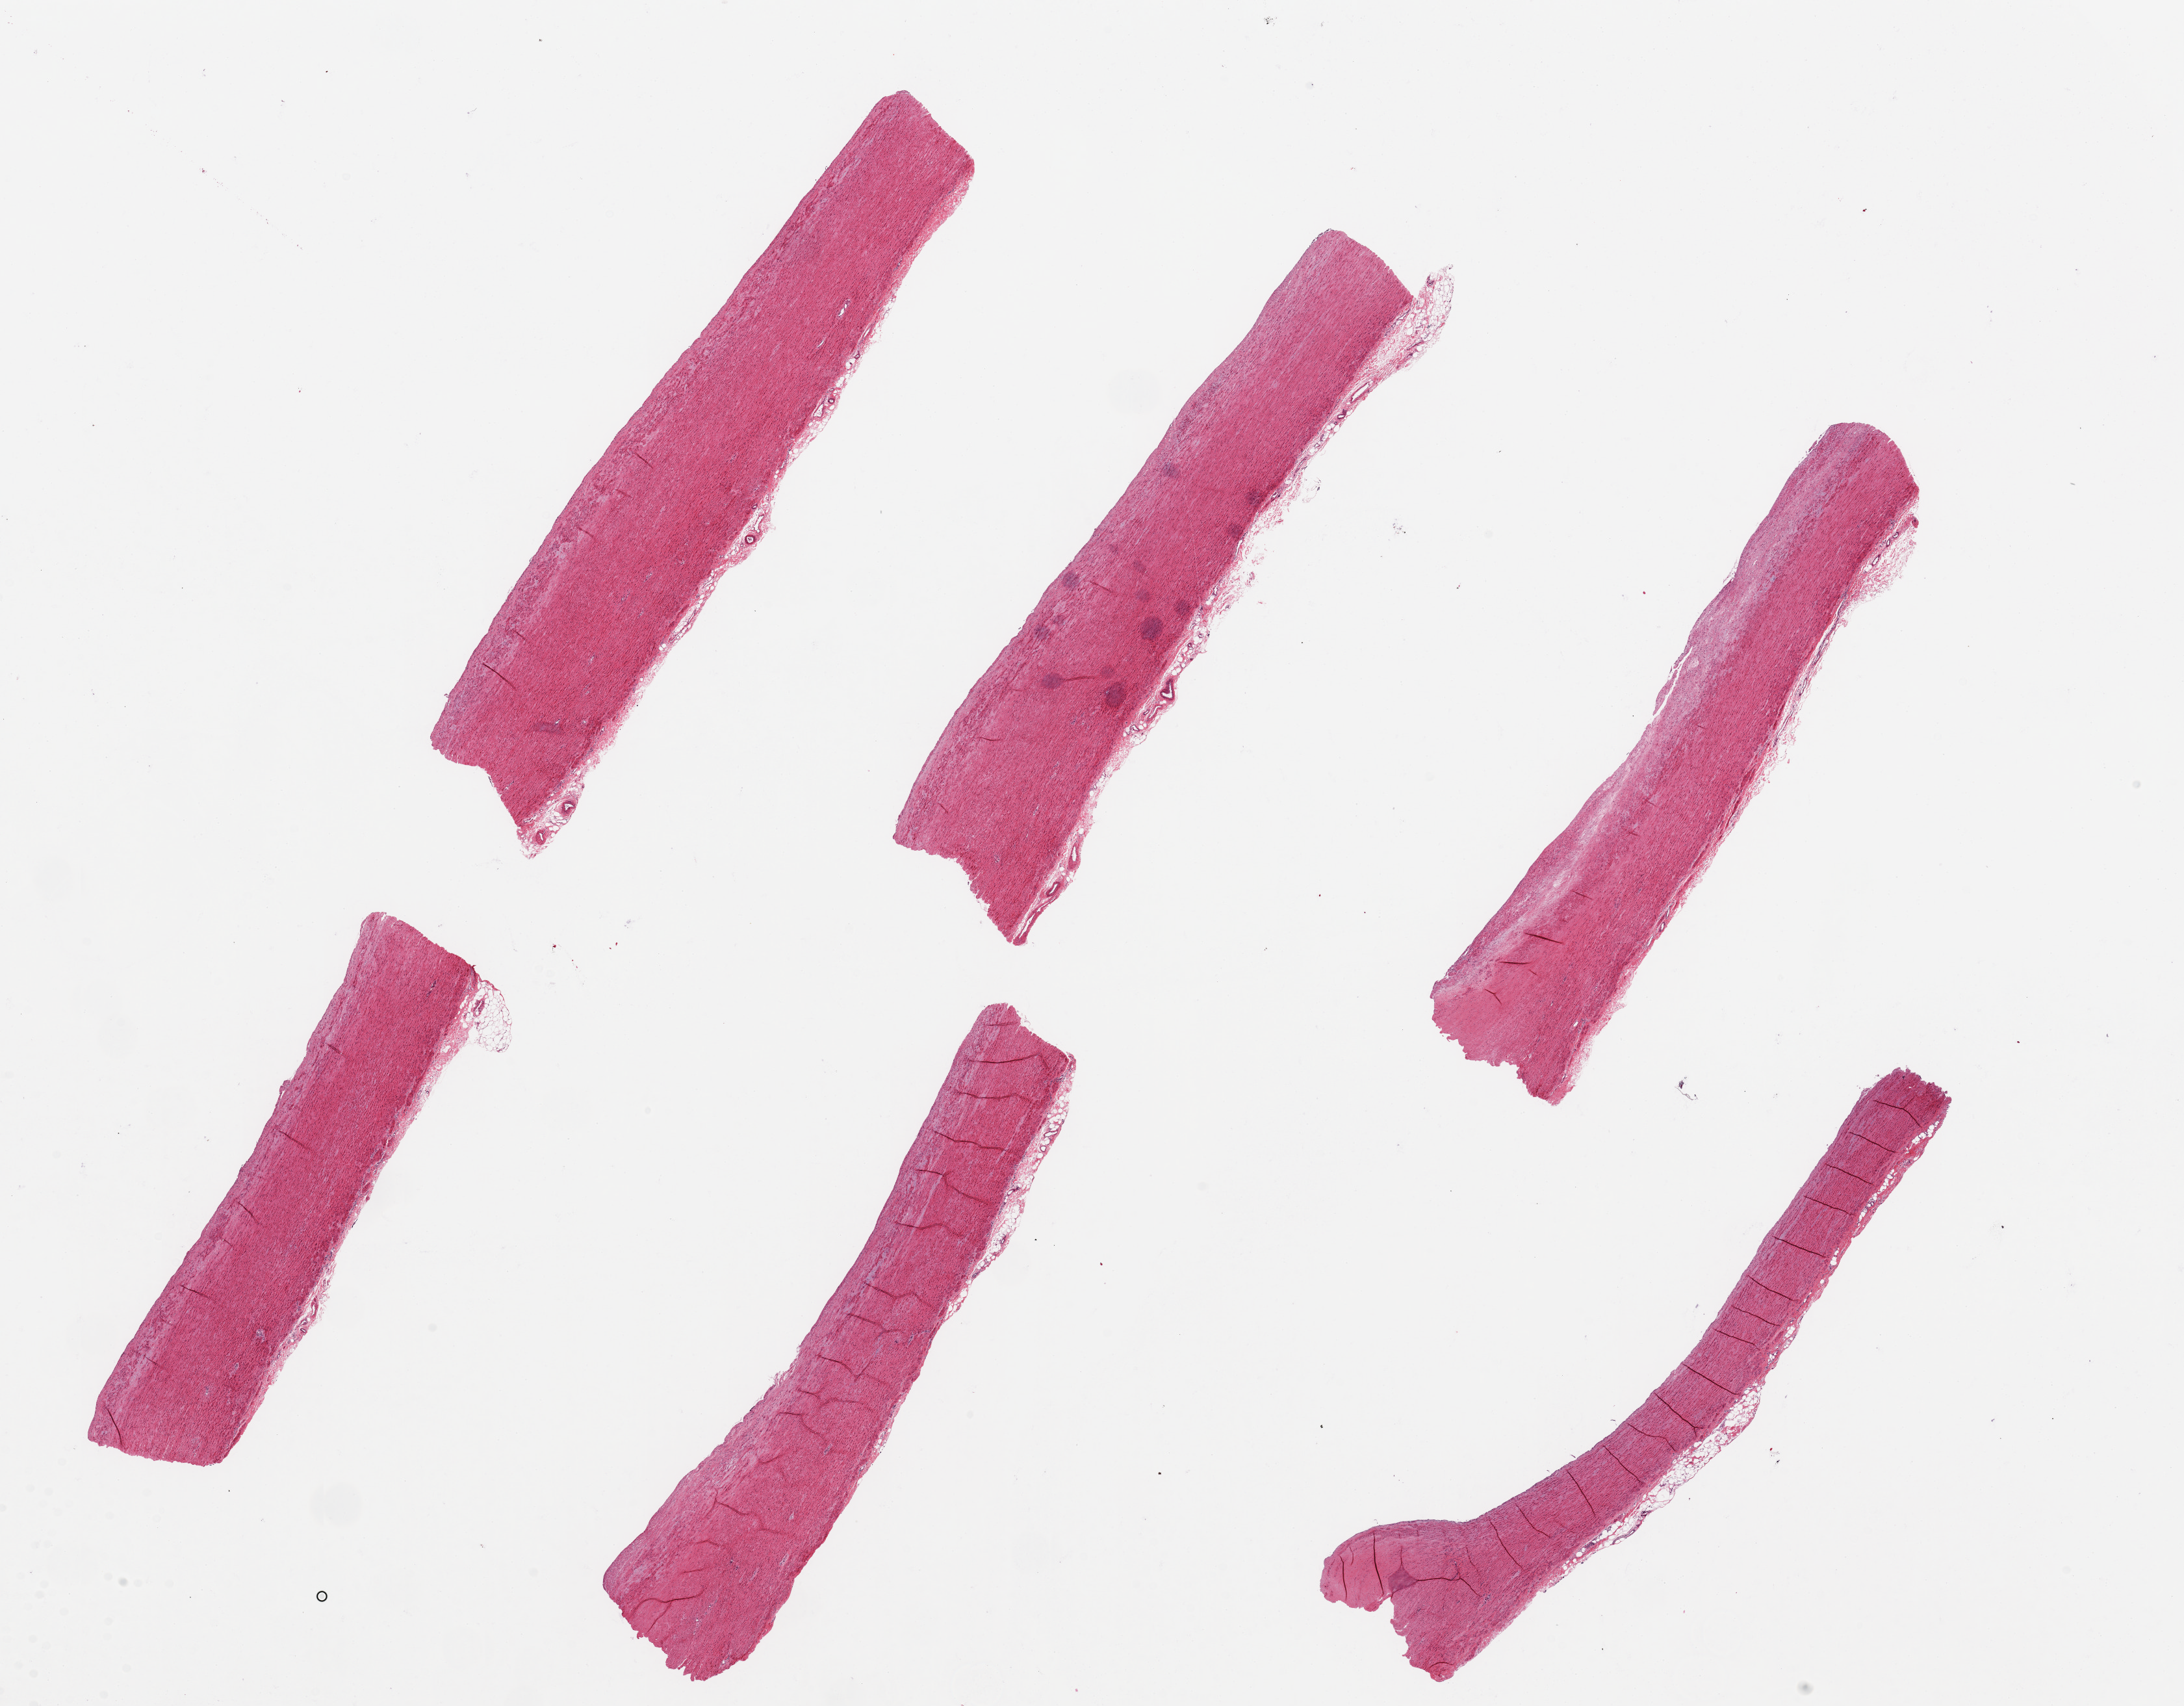
Hematoxylin and eosin (H&E) whole-slide image, whole scanned area (about 26.6 x 20.8 mm, acquisition: 20x scan) shown as a low-resolution overview, PAXgene-fixed, paraffin-embedded tissue, section of aorta (target tissue), tissue donor sample. Donor: male.
Pathologist's review note for this sample: 6 pieces ~10x2mm, some with up to ~ 0.5mm atherosis.